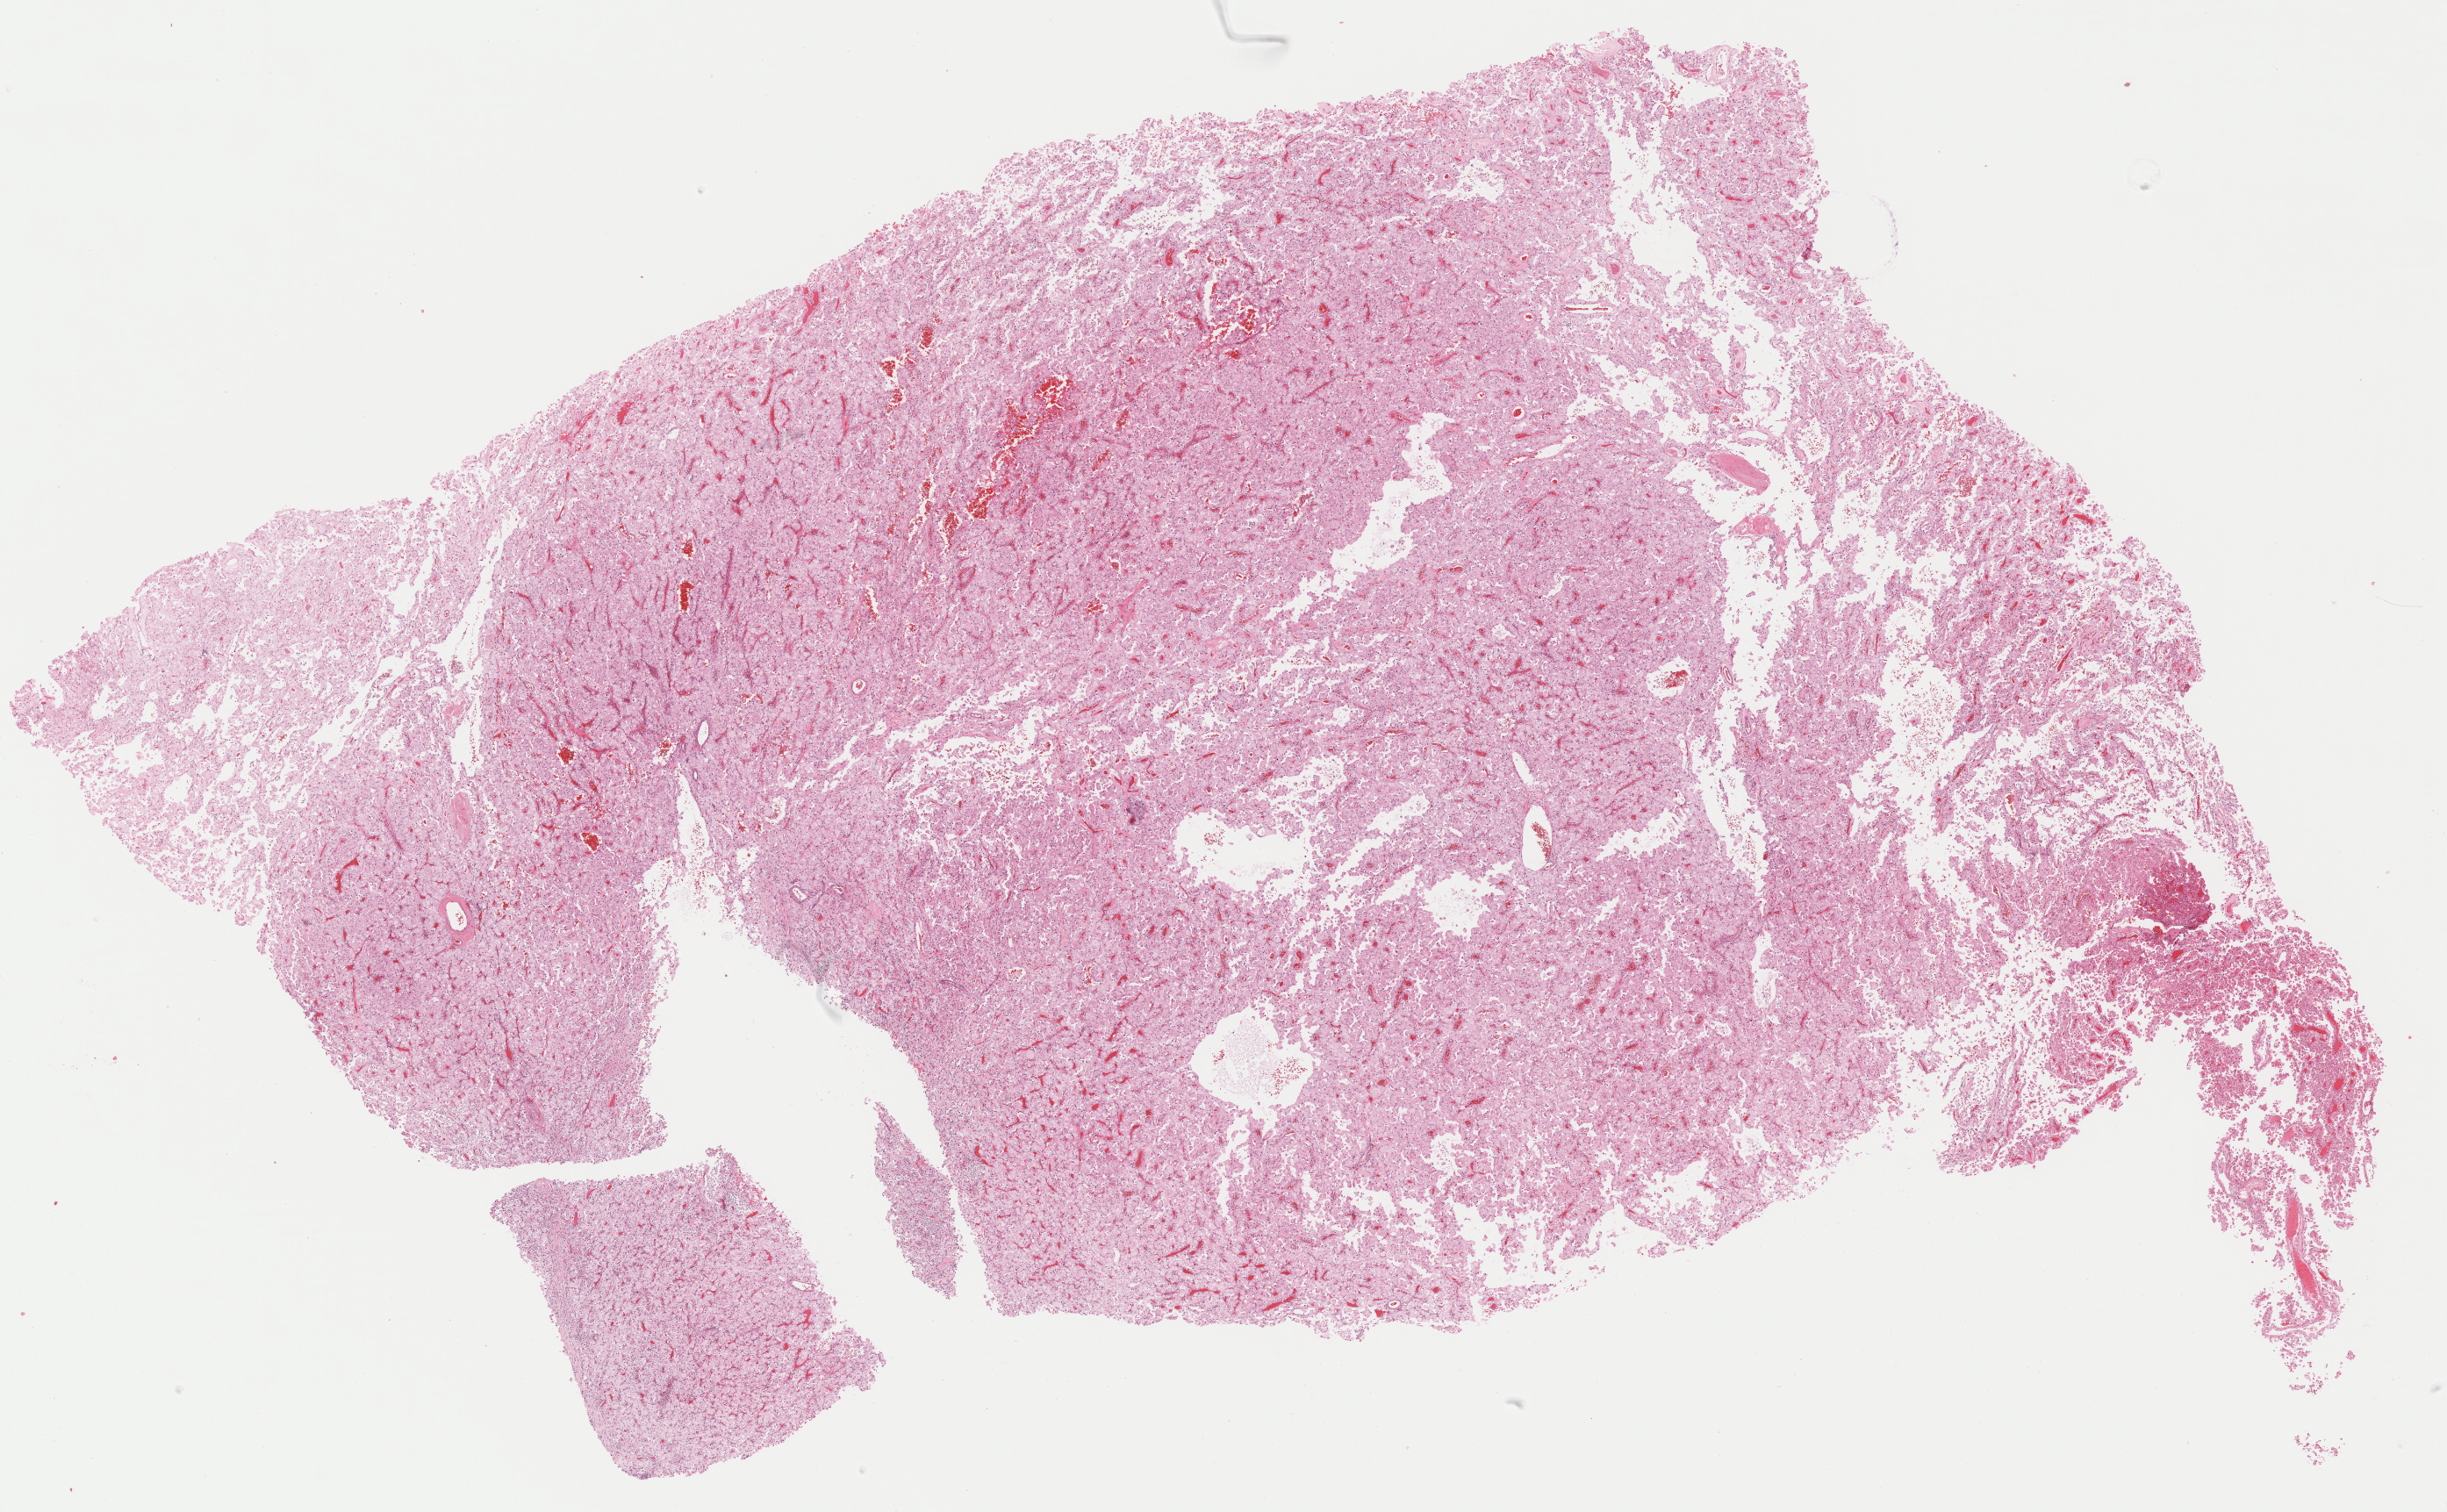
H&E-stained whole-slide image, shown as a low-resolution overview of the whole scanned area (about 22.5 x 13.9 mm), FFPE section, sample: primary tumour, kidney. Male, age 53 years at initial diagnosis.
- diagnosis: Renal cell carcinoma, chromophobe type
- TNM: T1b N0
- AJCC pathologic stage: I (6th edition)